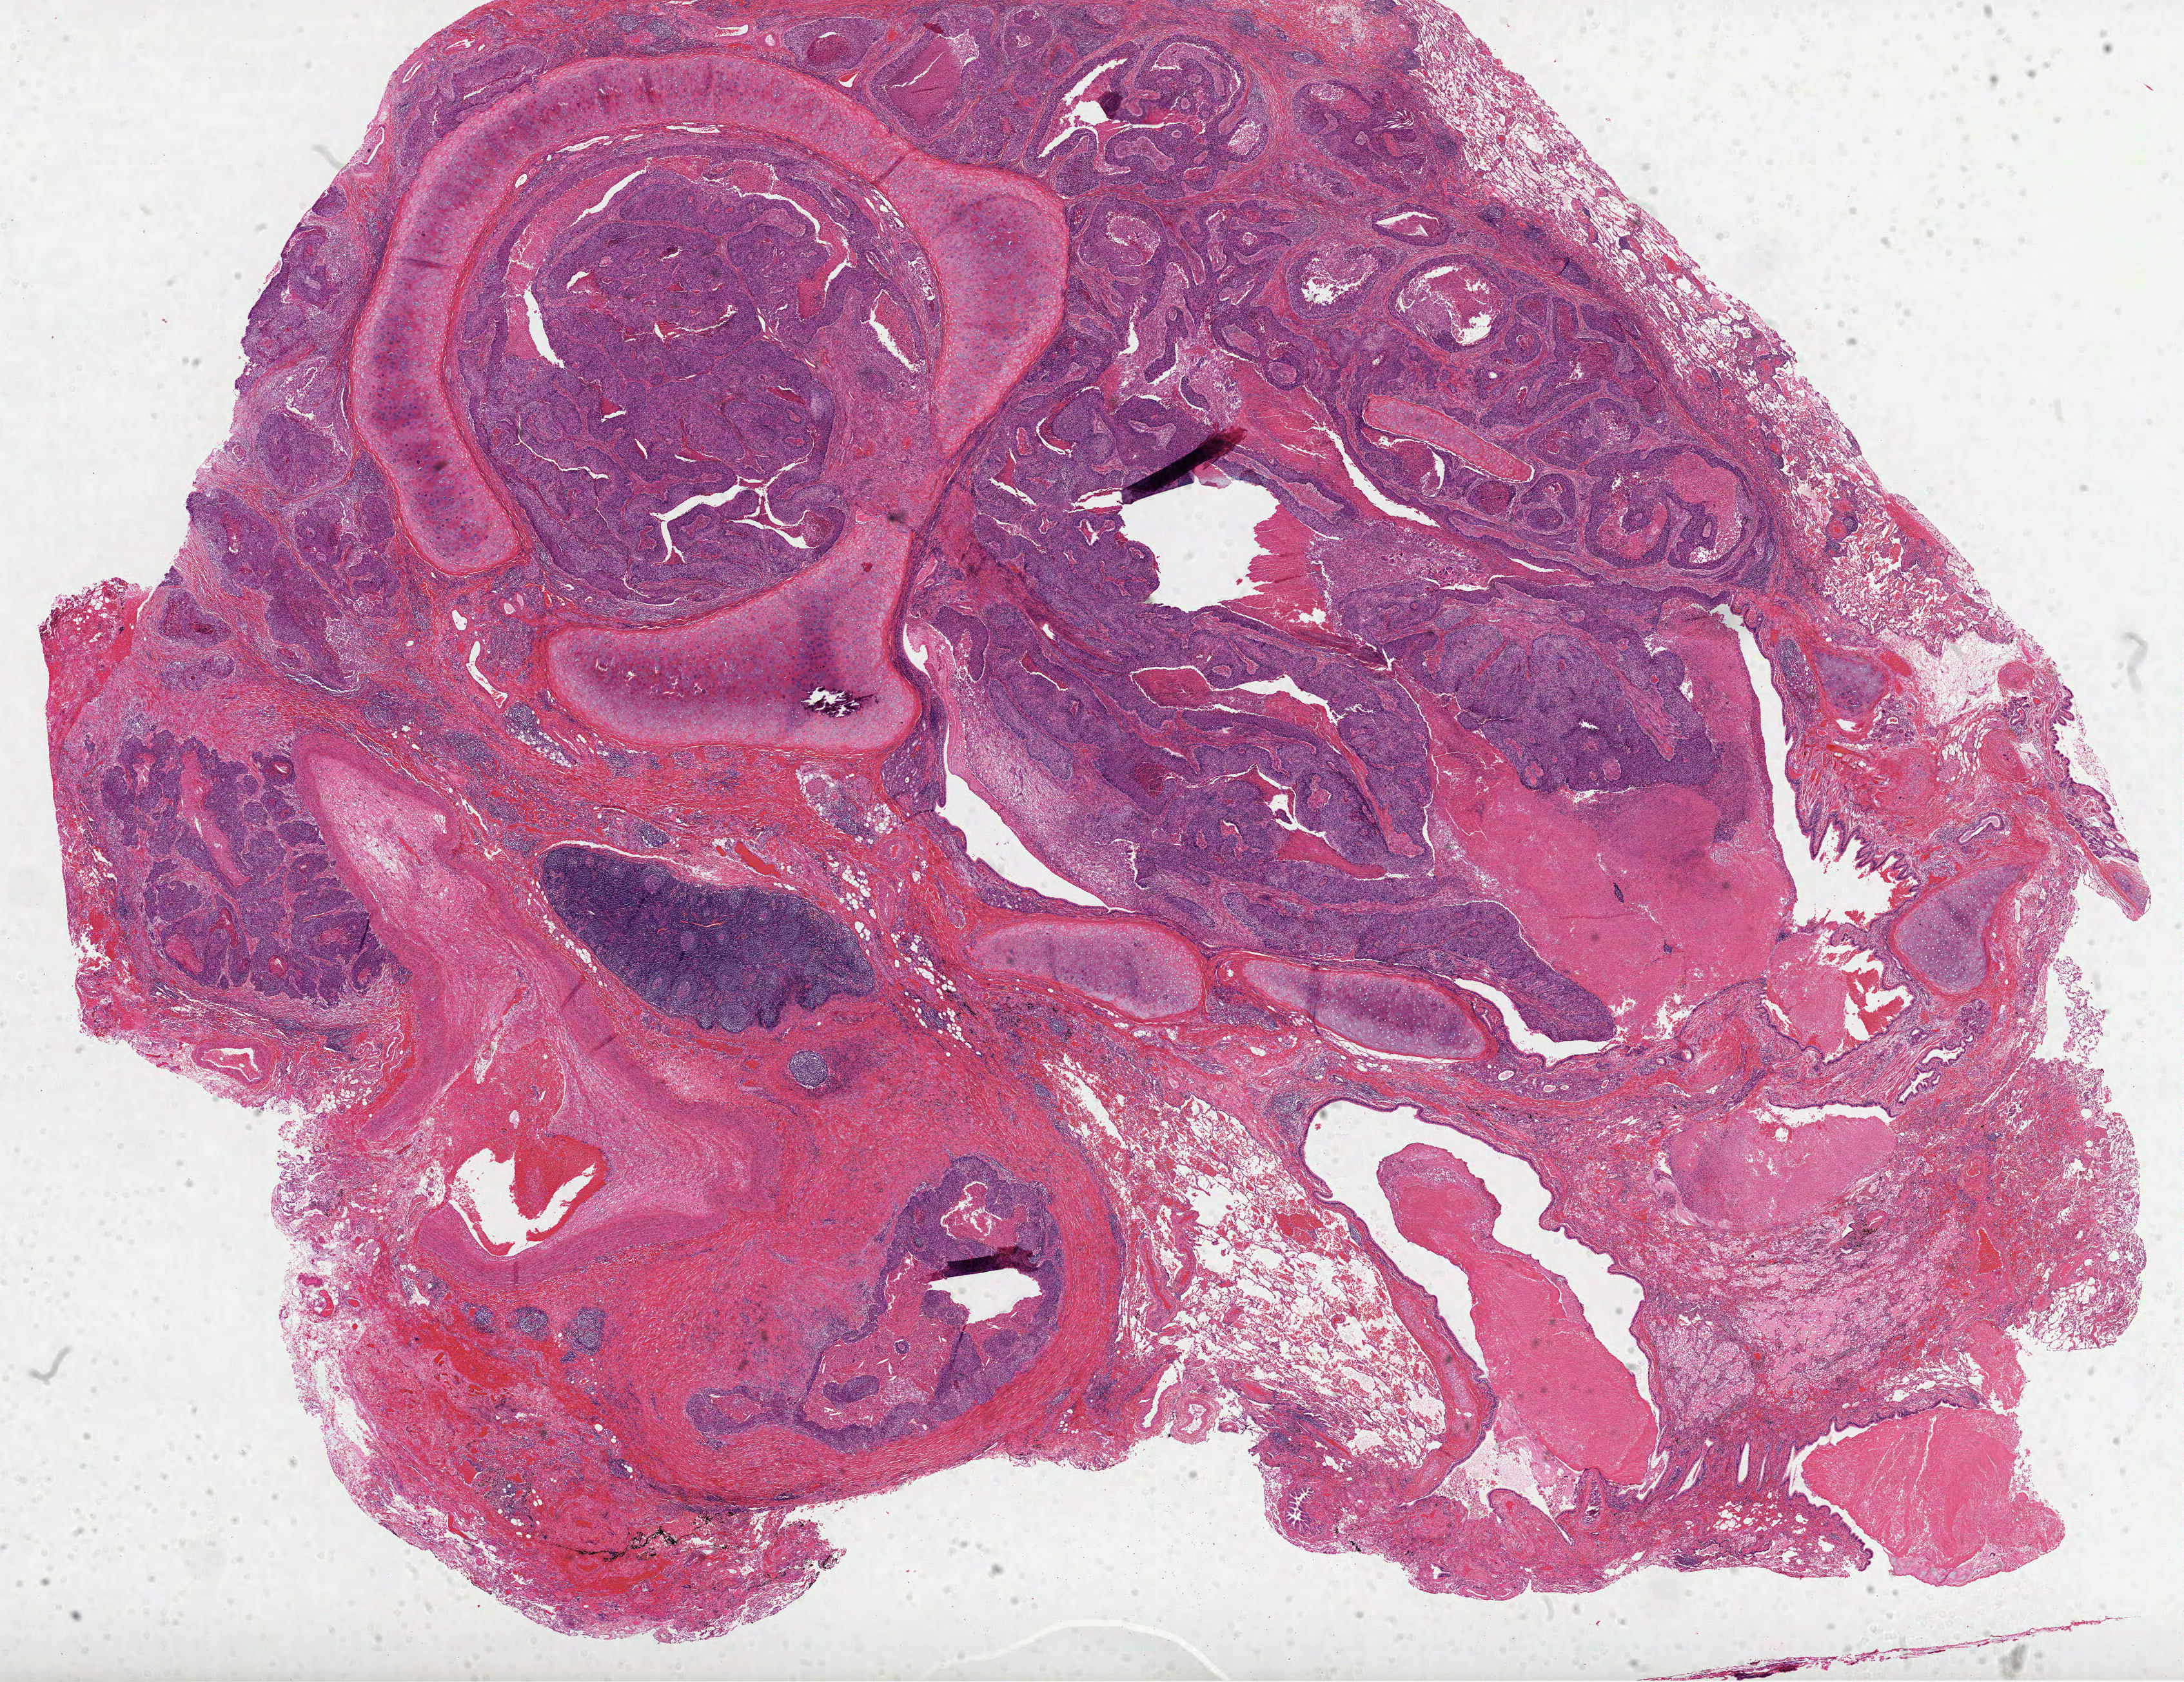
Whole-slide histology image, Hematoxylin and eosin (H&E) stained — a low-resolution overview of the entire scanned area, about 27.3 x 21.0 mm; FFPE section; sample: primary tumour, lung. Patient: male, age at initial diagnosis 56 years.
- diagnosis: Squamous cell carcinoma, NOS
- AJCC pathologic stage: IIB (6th edition)